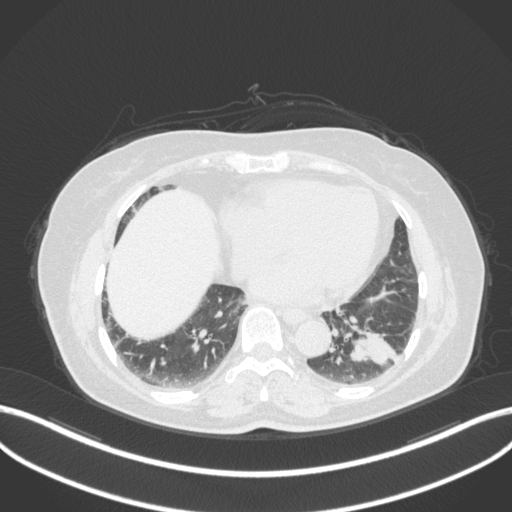
Chest CT, one axial slice; position 132 of 307 along the scan axis; reconstruction kernel B31f; 120 kVp; lung window (W 1500 / L -600 HU); 512 × 512 image matrix, field of view 400 × 400 mm. Female patient, age 59 years. From the clinical record (not read from this slice): clinical TNM (as recorded): T2a N0 M0; histopathological grade: G2-3.
Outlined on this slice (bounding box drawn by a radiologist):
- lung tumour (recorded histology: adenocarcinoma): bounding box (x1, y1, x2, y2) in pixels: (348, 325, 398, 367)